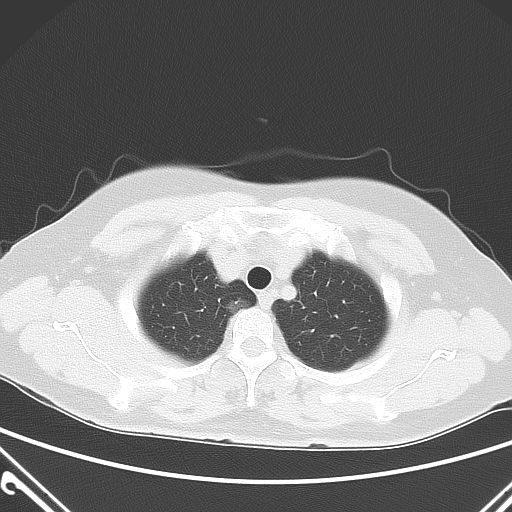
Chest CT, one axial slice. Position 49 of 60 along the scan axis. 120 kVp. Lung window (W 1500 / L -600 HU). 5 mm slice thickness. 512 × 512 image matrix, field of view 350 × 350 mm. Patient: female, 54 years. From the clinical record (not read from this slice): clinical TNM (as recorded): T1a N0 M0; histopathological grade: G1.
Annotated regions visible in this slice (rectangle marked by the reading radiologist):
- lung tumour (recorded histology: adenocarcinoma): box from (x=222, y=292) to (x=254, y=324) px